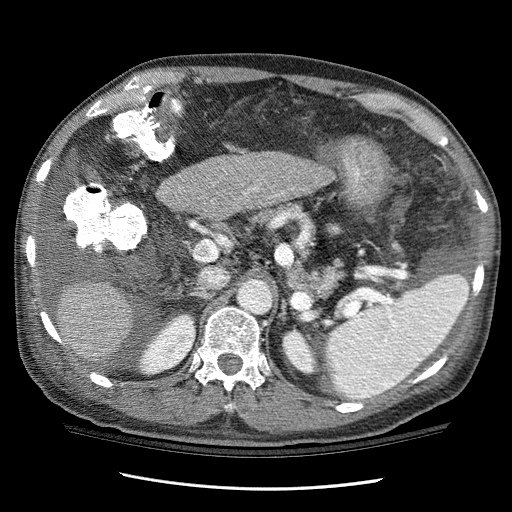
Contrast-enhanced abdominal CT (liver protocol), one axial slice; slice 61 of 114 in the series (ordered by position); 120 kVp; one of 3 acquisitions stored at this slice position; soft-tissue window (W 400 / L 40 HU); 512 × 512 image matrix. Case-level facts recorded for this patient, not image findings: diagnosis: hepatocellular carcinoma (patient treated with transarterial chemoembolisation; whether this scan precedes or follows treatment is not stated here); TNM stage (as recorded): Stage-I; Child-Pugh class: C.
Outlined on this slice (semi-automatic segmentation, software-assisted and operator-edited):
- liver parenchyma outside the tumour (the mass and vessels are separate outlines, so this box may not span the whole liver): bounding box (x1, y1, x2, y2) in pixels: (52, 150, 330, 365)